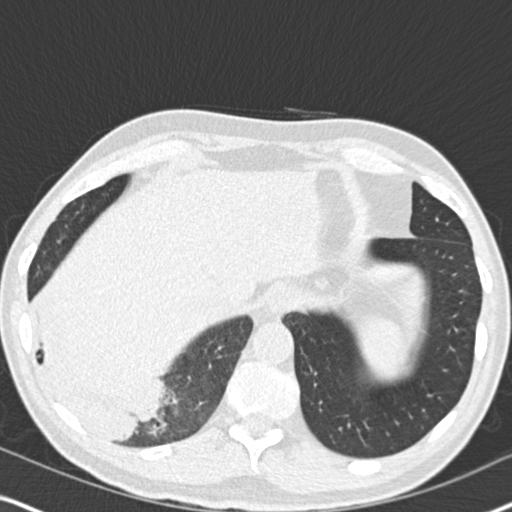
Chest CT (low-dose screening protocol), one axial image. Second annual screen. Lung window (W 1500 / L -600 HU). Slice 133 of 182 in the series. 512 × 512 image matrix, field of view 330 × 330 mm. Male, age 61 years at enrolment. Current smoker at enrolment.
Lesion marked by an expert reader, bounding box [x1, y1, x2, y2] px = [17, 276, 180, 454]. Reader record for this screening exam (exam-level; its link to the box is not recorded): non-calcified nodule or mass ≥4 mm, right lower lobe, 90 × 80 mm, soft tissue attenuation, pre-existing on the prior screen: yes; interval growth: yes. Official screen result: positive, other. Lung cancer was diagnosed 20 days after this screen: bronchiolo-alveolar adenocarcinoma, NOS, right lower lobe, moderately differentiated (G2), stage IIIB (AJCC 6th edition), 90 mm at pathology.